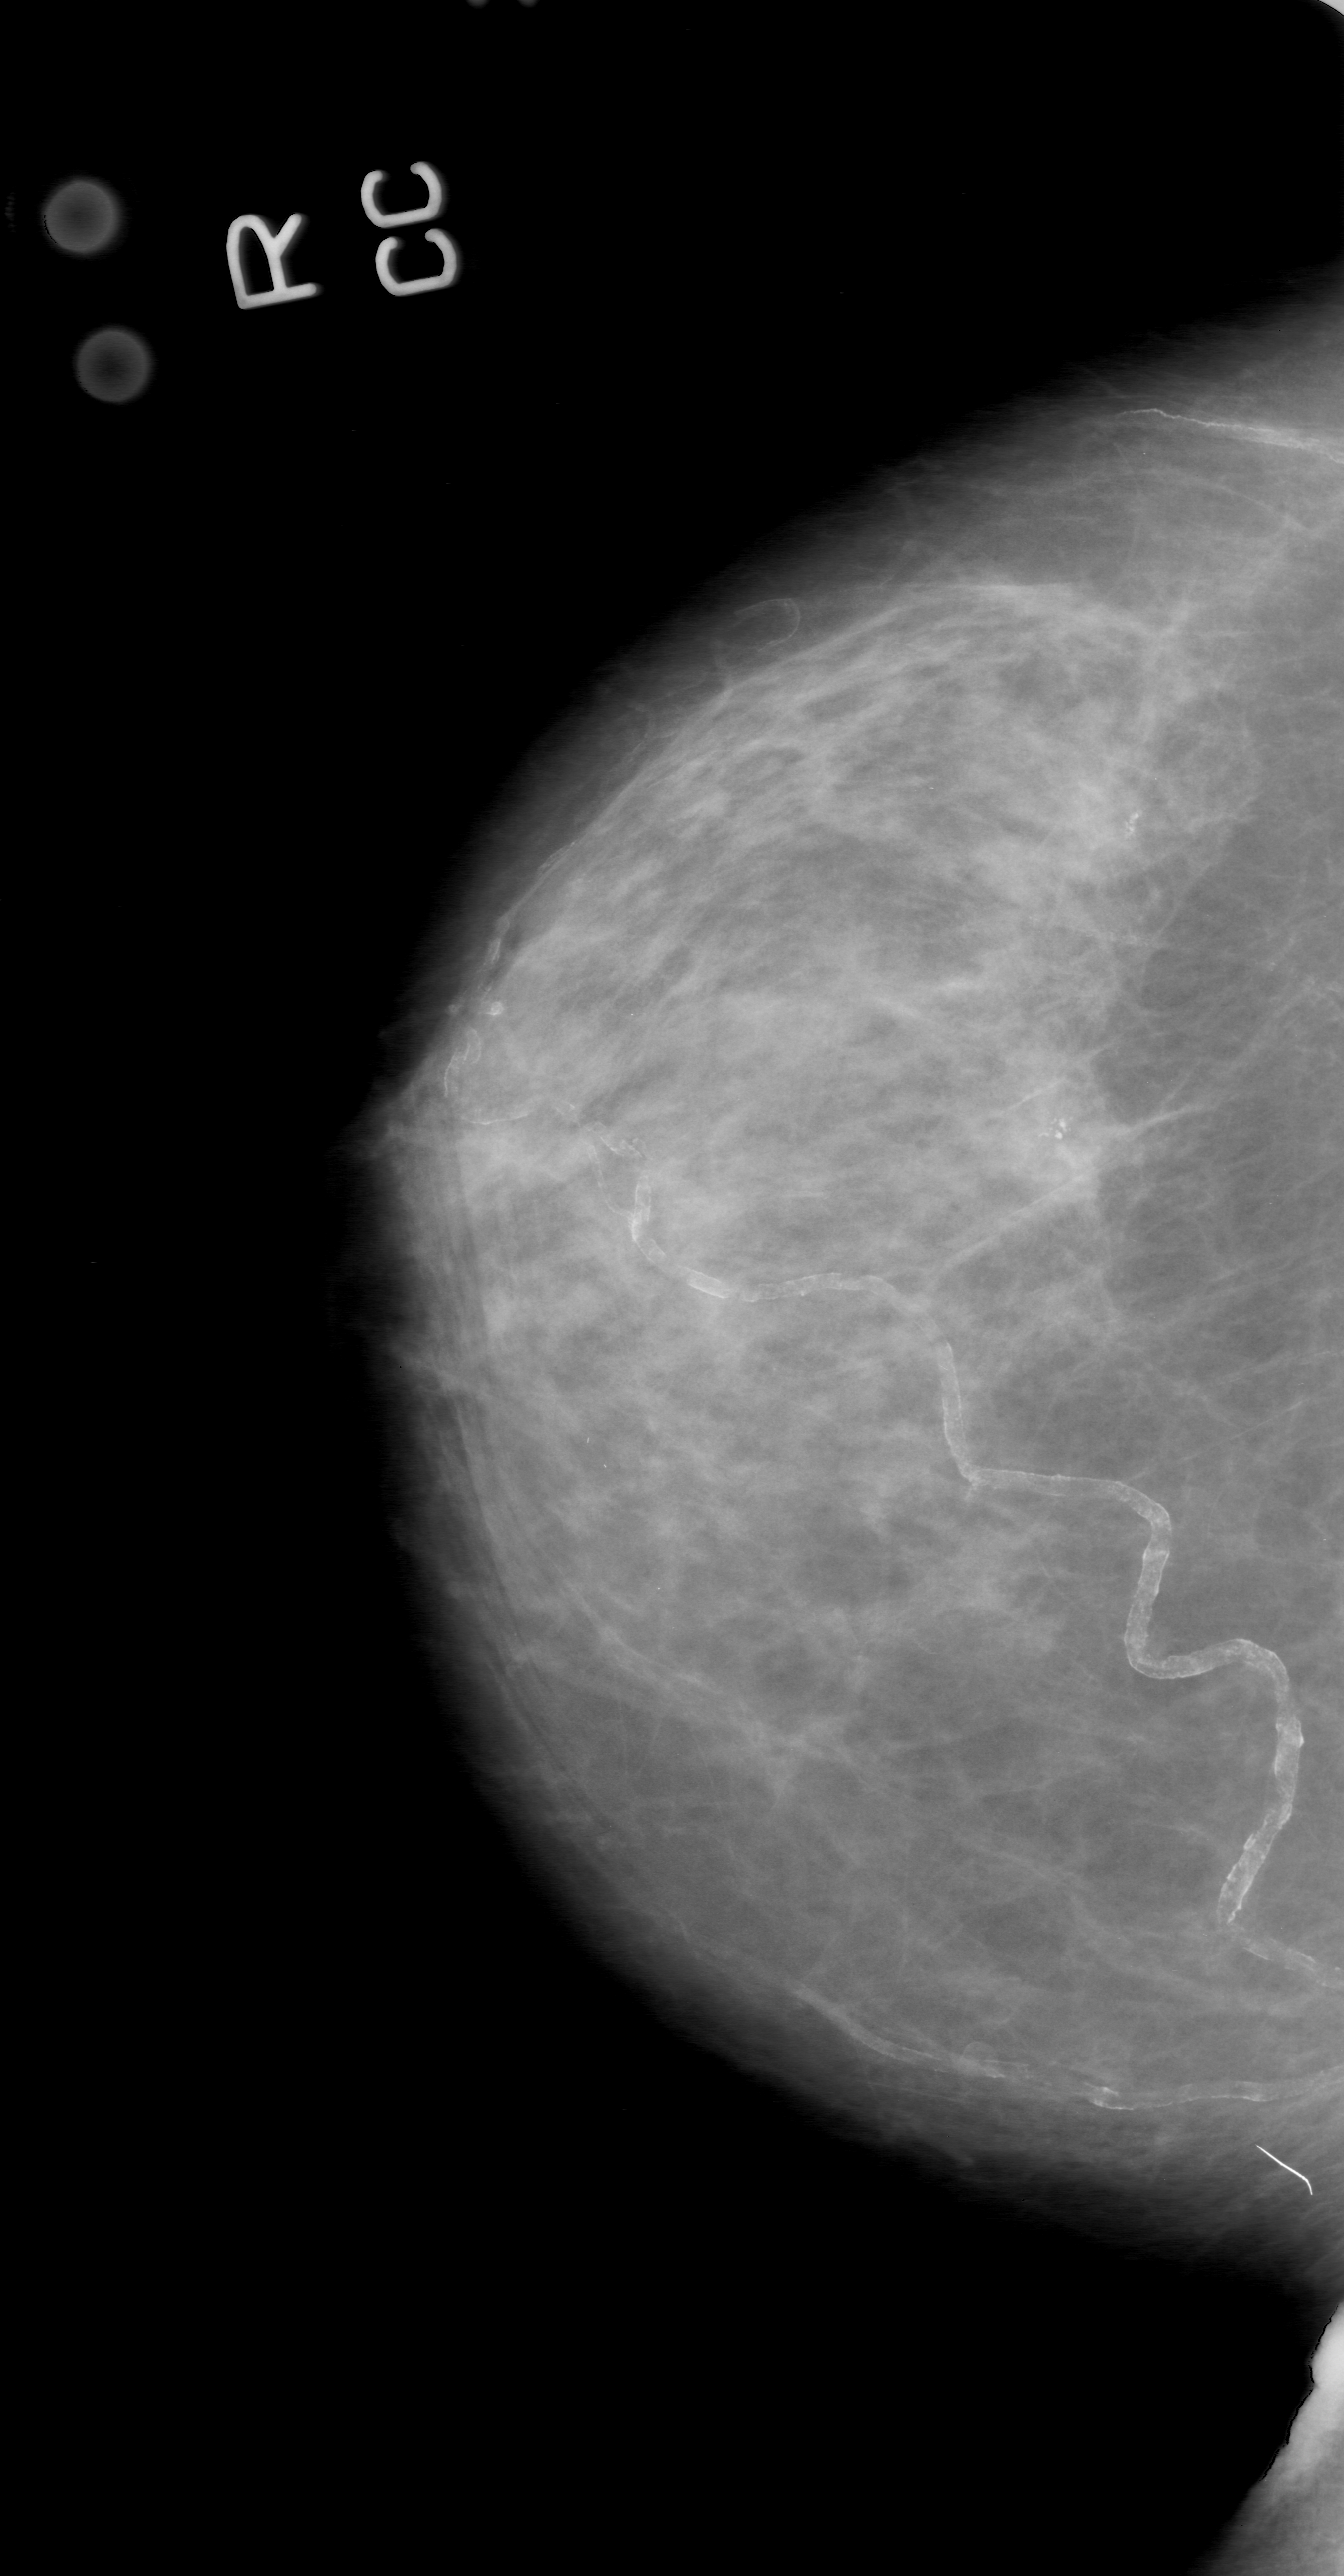
Digitized screen-film mammogram. Right breast. Craniocaudal (CC) view. BI-RADS breast density category 3 (scale 1–4). 1344 × 2576 image matrix.
Expert-marked regions of interest on this film, with their recorded descriptors:
- calcifications, morphology coarse, distribution clustered; BI-RADS assessment category 0 (incomplete: needs additional imaging); pathology (as recorded): benign: bounding box [x1, y1, x2, y2] px = [945, 1059, 1120, 1227]